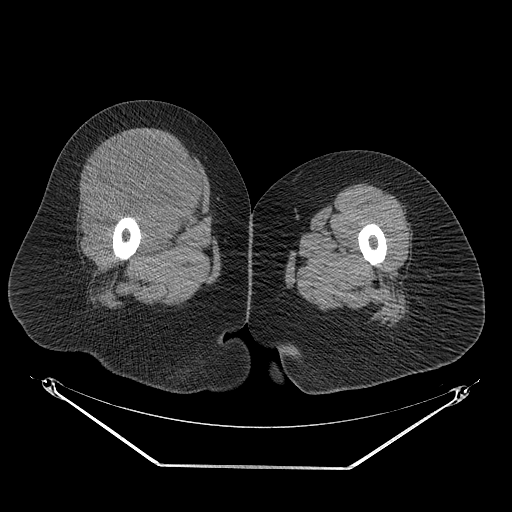
CT of an extremity soft-tissue mass (from a PET/CT study), one axial slice; position 37 of 267 along the scan axis; reconstruction kernel STANDARD; soft-tissue window (W 400 / L 40 HU); 3.75 mm slice thickness; 512 × 512 image matrix. Female patient. Case-level facts recorded for this patient, not image findings: histological type: malignant solitary fibrous tumor; grade: intermediate; site of the primary tumour: right thigh.
Structures marked on this image (expert contour drawn on MRI and transferred to this co-registered scan by the dataset authors):
- gross tumour volume including surrounding oedema: bounding box <85,133,209,229> (left, top, right, bottom; pixels)
- gross tumour volume (mass): <89,135,204,225>